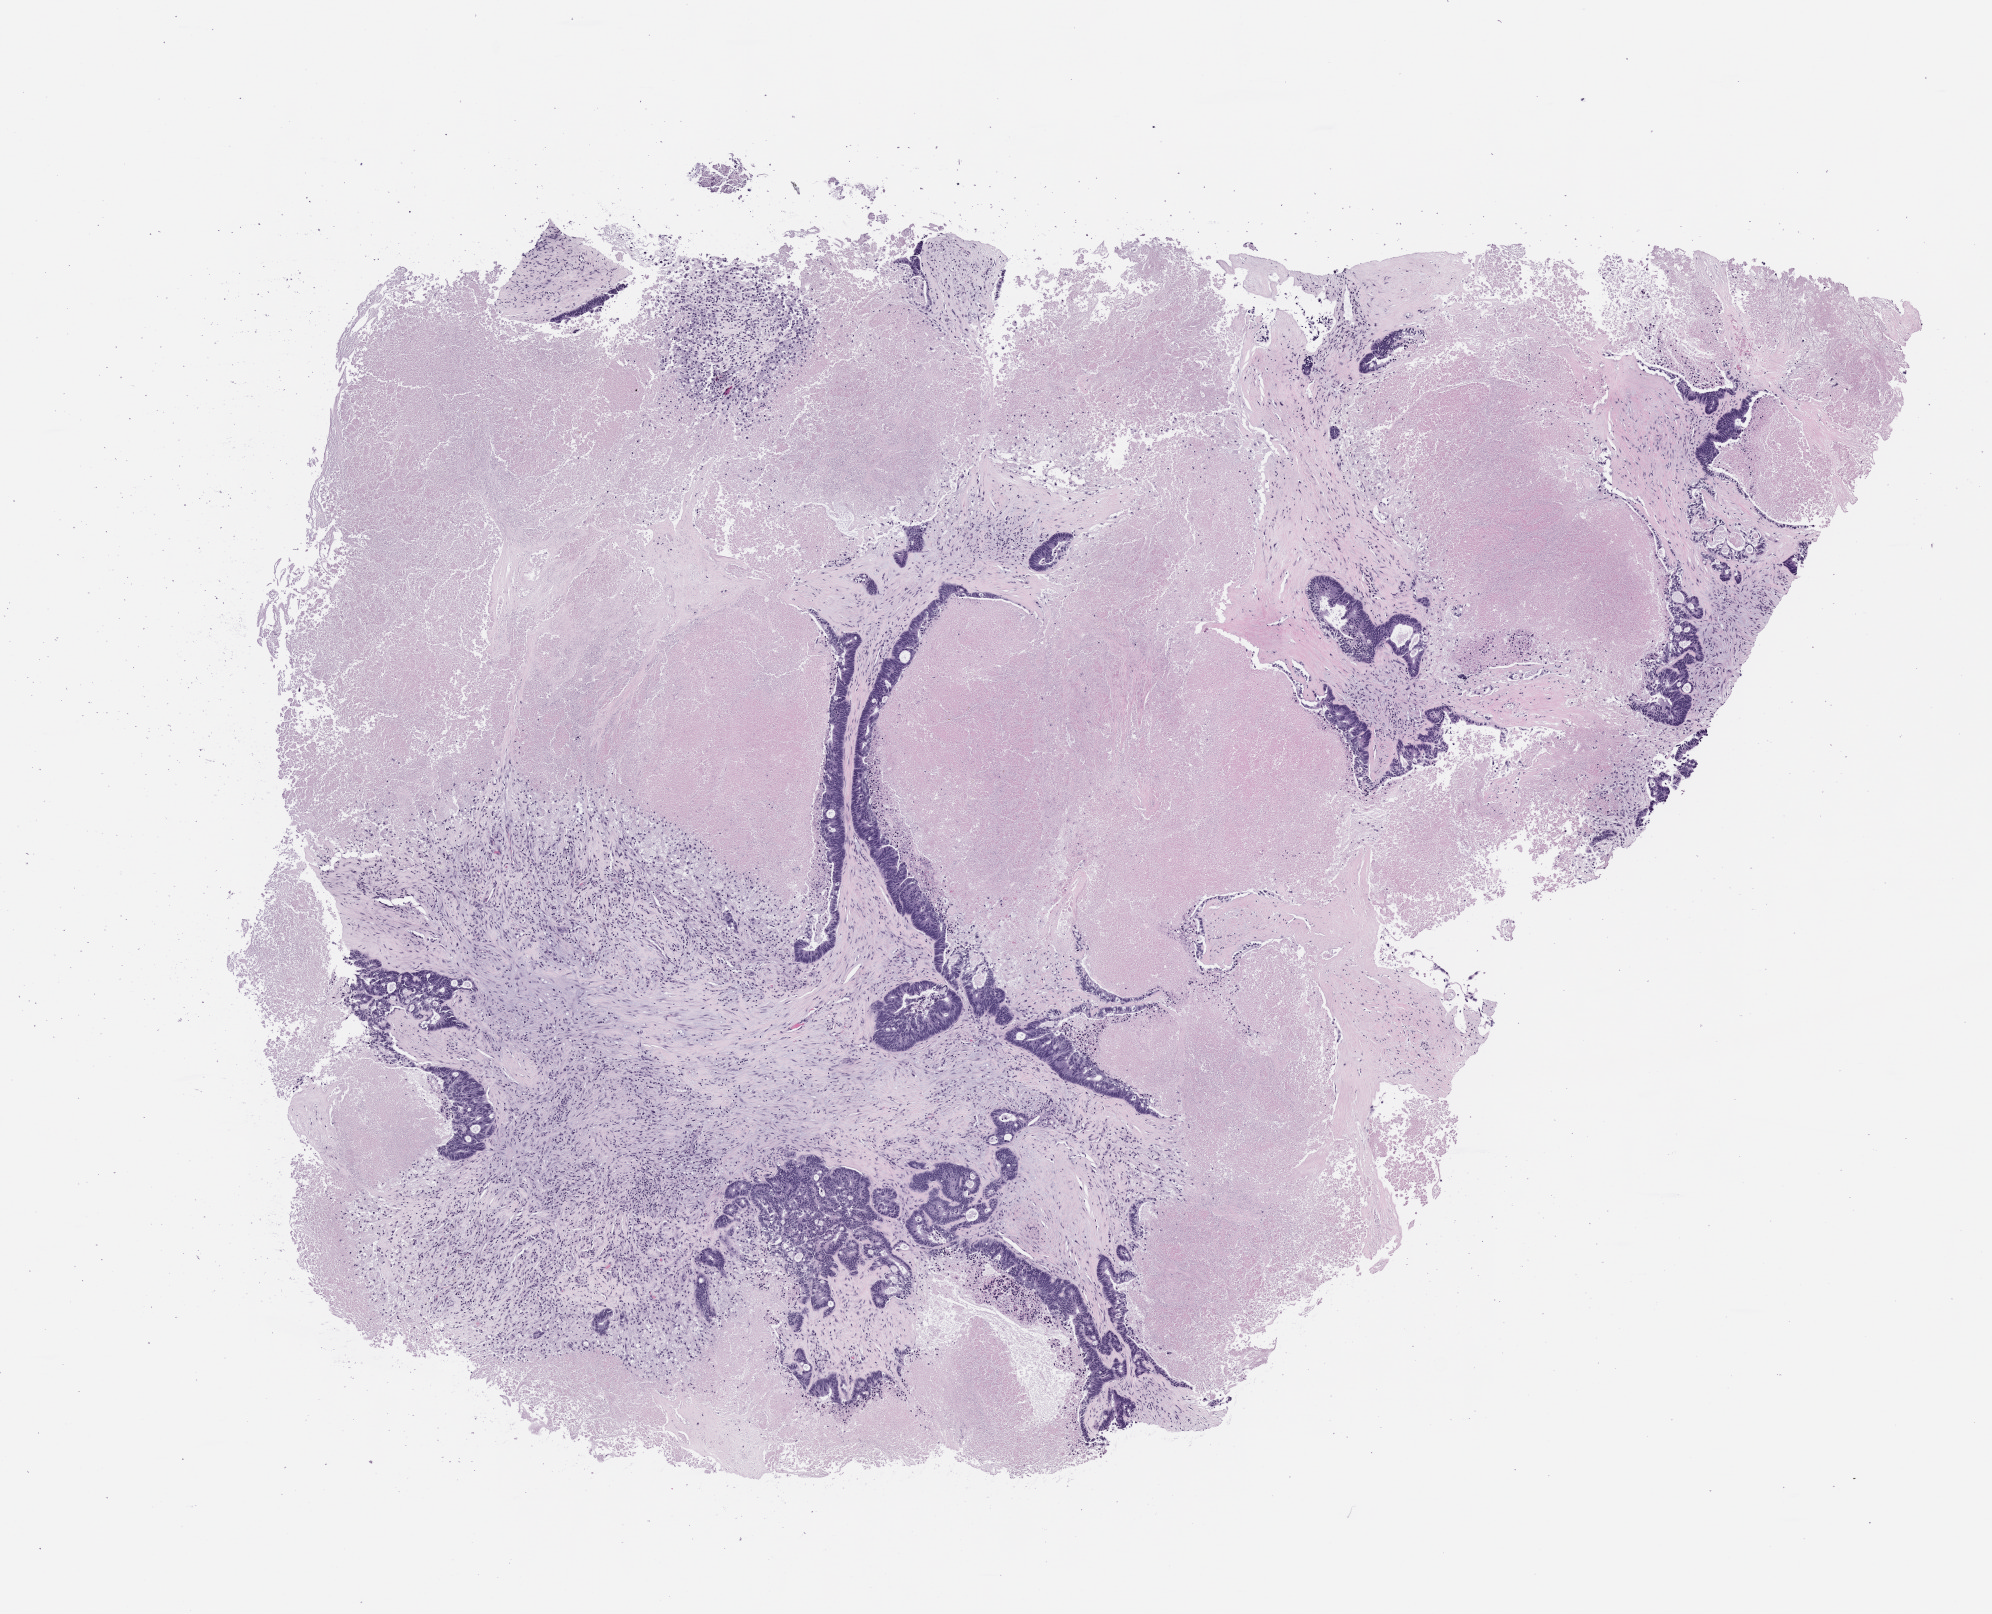
Digitized H&E-stained section of the patient's (originator) tumor tissue — a low-resolution overview of the entire scanned area, about 8.0 x 6.5 mm, FFPE section, originating tumor site category: gastrointestinal tract. Patient sex: female.
Diagnosis: Colorectal Carcinoma.